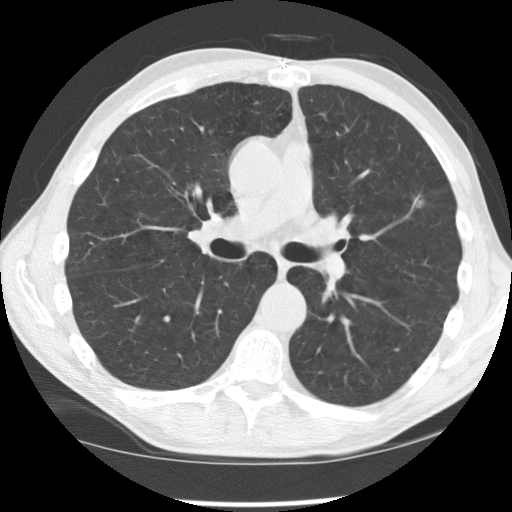
Axial slice from a low-dose chest CT screening exam, second screening round (one year after baseline), lung window (W 1500 / L -600 HU), 120 kVp, 512 × 512 image matrix. Male, age 64 years at enrolment.
• Lesion marked by an expert reader, bounding box <390,180,446,225> (left, top, right, bottom; pixels).
• The exam's reader record, not a measurement of the box and not confirmed to be the same lesion: non-calcified nodule or mass ≥4 mm, left upper lobe, 16 × 11 mm, spiculated (stellate) margins, soft tissue attenuation, pre-existing on the prior screen: yes; interval growth: yes.